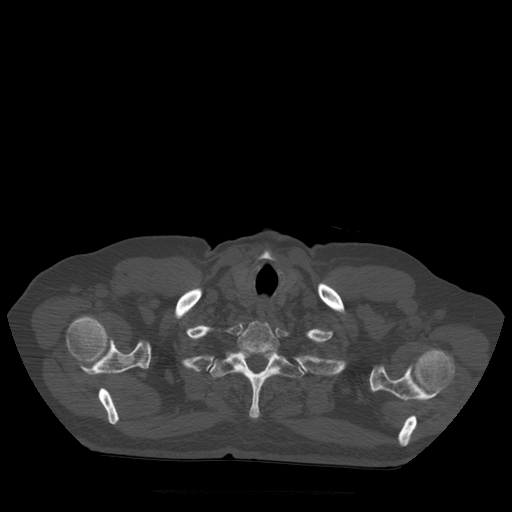
CT including the spine, one axial slice; slice 431 of 522 in the series (ordered by position); bone window (W 1800 / L 400 HU); 1.25 mm slice thickness; 512 × 512 image matrix, field of view 420 × 420 mm. Patient age 72 years. Case-level facts recorded for this patient, not image findings: primary cancer: prostate.
Outlined on this slice (semi-automatically segmented with operator editing):
- T1 vertebra: bounding box [x1, y1, x2, y2] px = [238, 322, 280, 354]
- T2 vertebra: [210, 350, 305, 419]